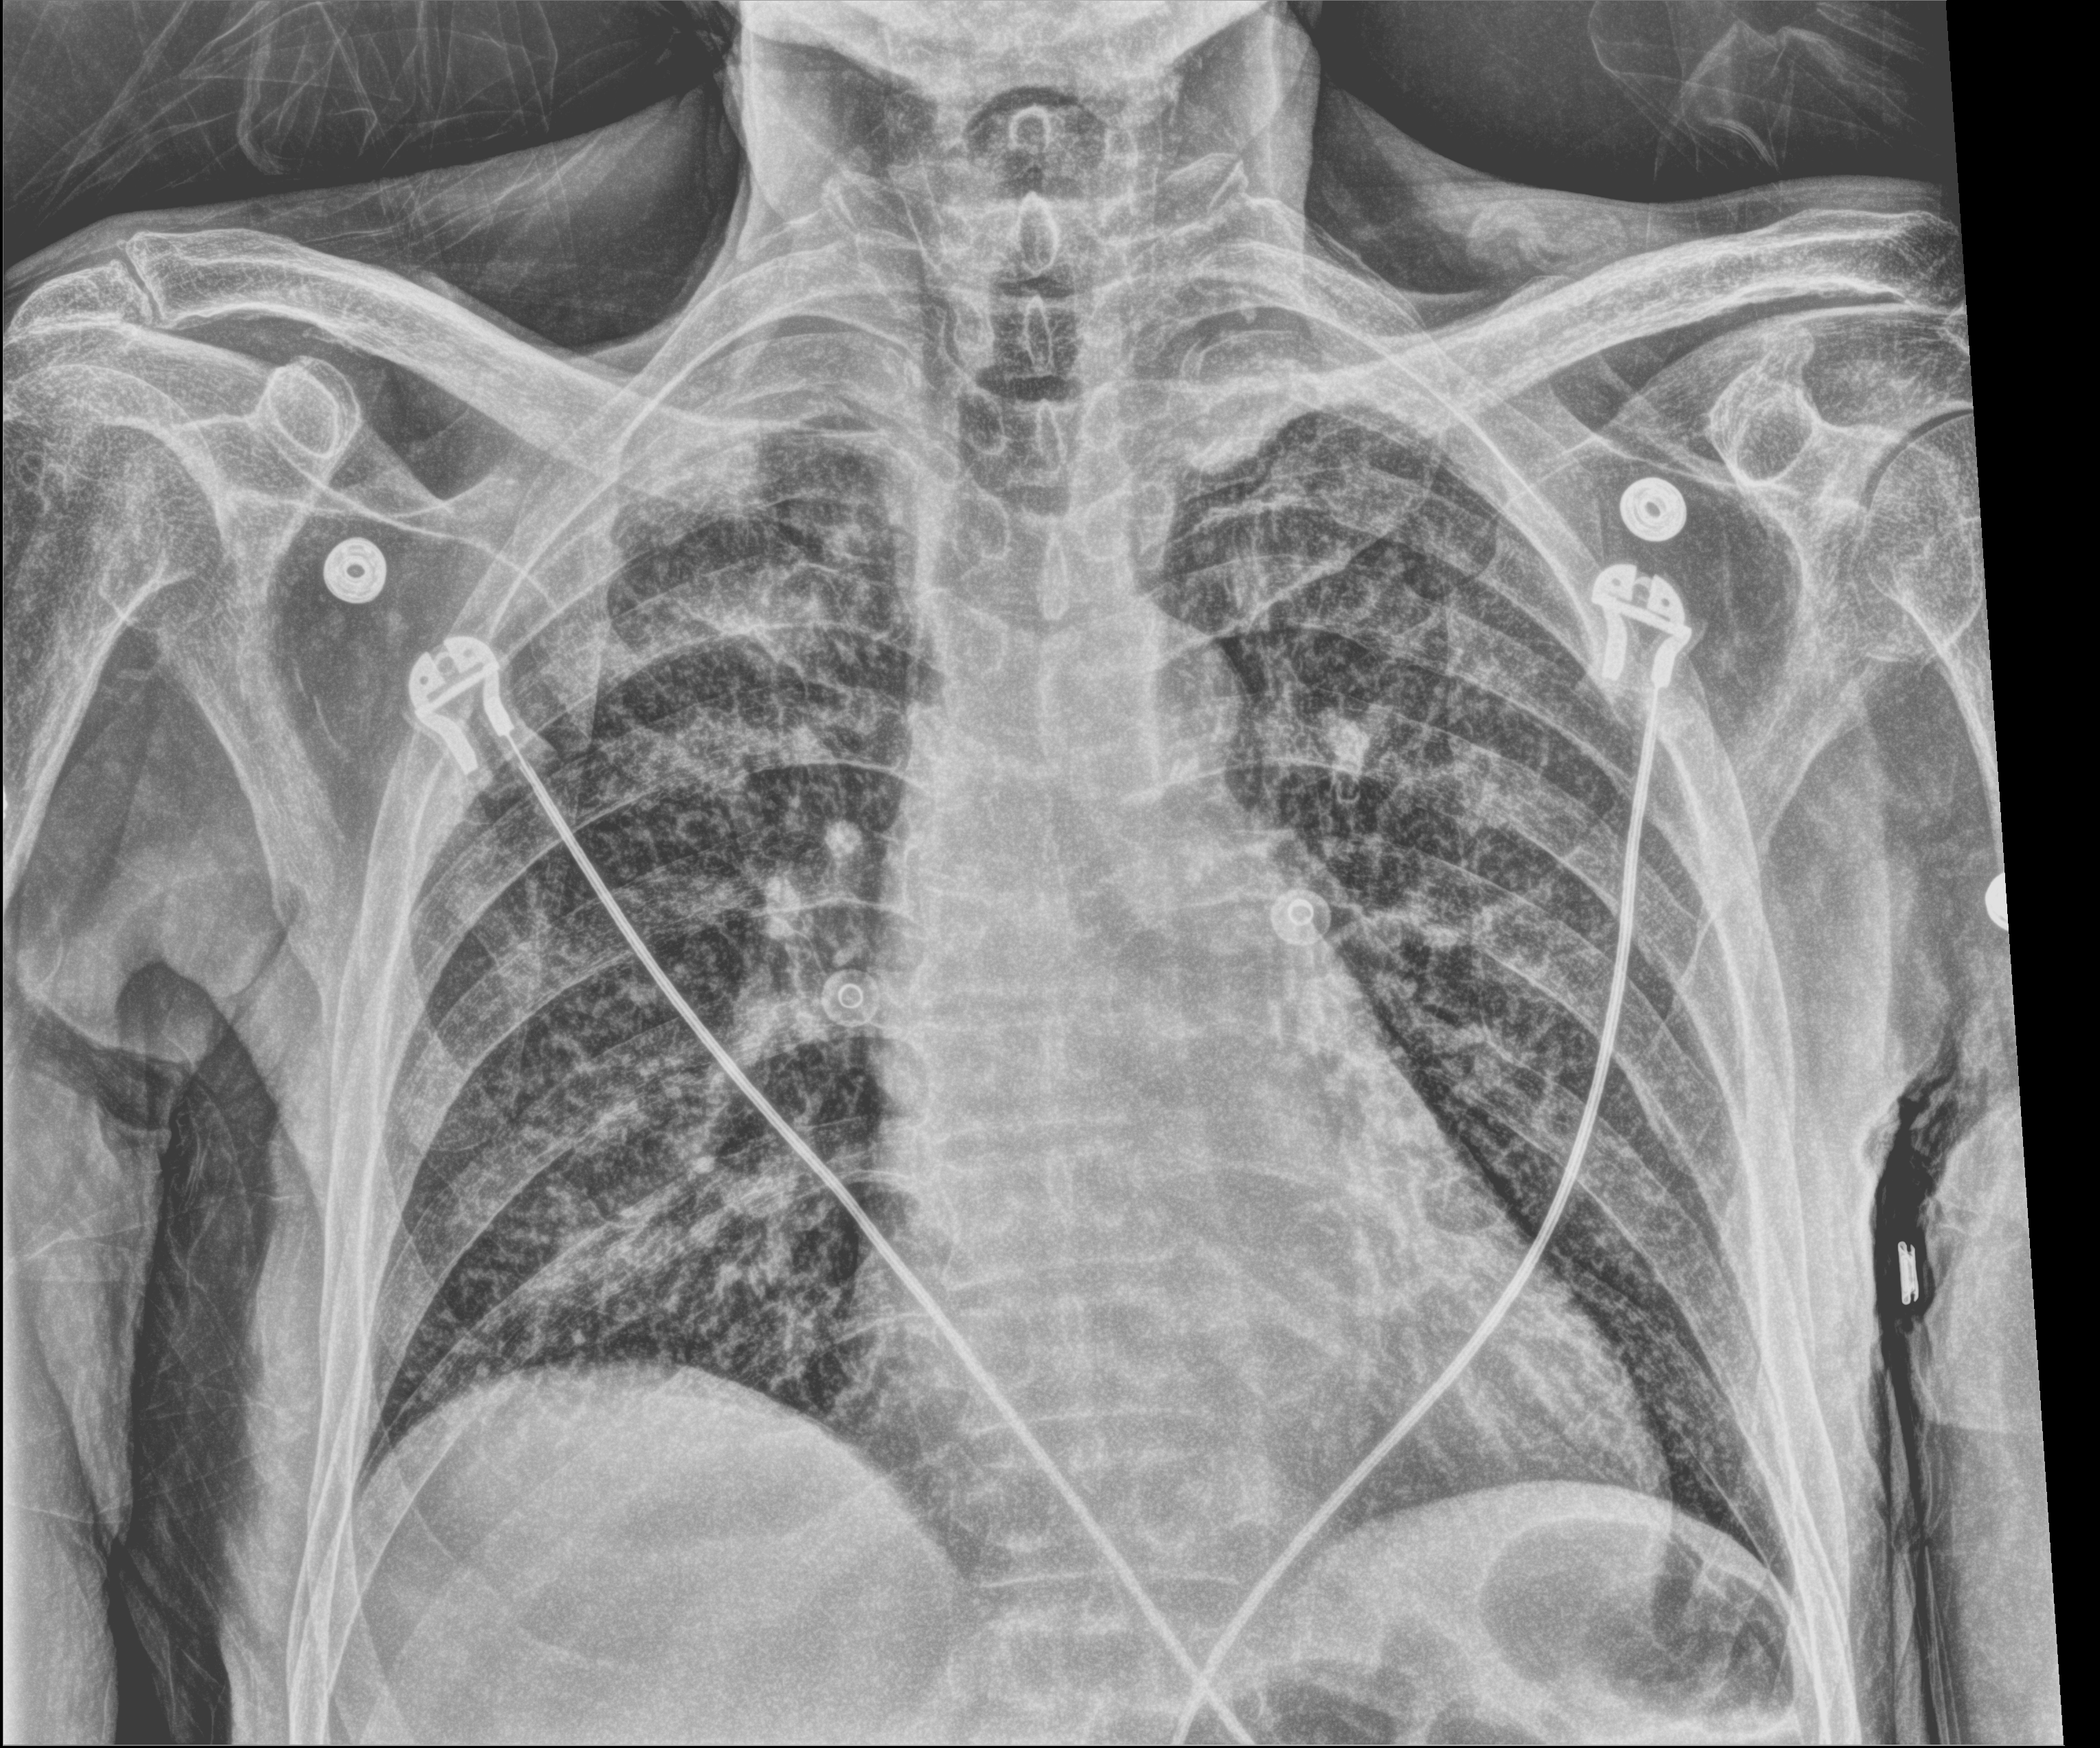
Bedside chest radiograph (computed radiography); anteroposterior (AP) projection. Patient hospitalised with COVID-19; male, aged 75–90 years.
Admission-level facts for this patient (not findings on this image; timing relative to this image not recorded): length of hospital stay: 14 days.